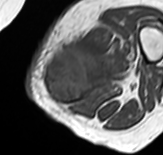
MRI of an extremity soft-tissue mass, one axial slice. Slice 20 of 65 in the series (ordered by position). MR volume resampled by the dataset authors to the PET/CT grid (not the native acquisition matrix). 3.27 mm slice thickness. 163 × 155 image matrix, field of view 159 × 151 mm. Female patient. Case-level facts recorded for this patient, not image findings: histological type: pleomorphic leiomyosarcoma; grade: high; site of the primary tumour: left thigh.
Outlined on this slice (expert contour drawn on MRI and transferred to this co-registered scan by the dataset authors):
- gross tumour volume including surrounding oedema: bounding box [x1, y1, x2, y2] px = [44, 28, 129, 105]
- gross tumour volume (mass): [44, 49, 109, 103]